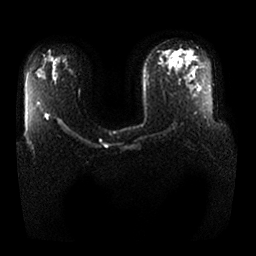
Breast MRI, one axial slice; position 12 of 25 along the scan axis; diffusion-weighted series; image 2 of 4 stored at this slice position (different b-values; order by instance number); 1.5 T; 4 mm slice thickness; 256 × 256 image matrix, field of view 380 × 380 mm. Female patient.
Annotated regions visible in this slice (expert manual segmentation):
- tumour on diffusion-weighted imaging: box from (x=46, y=114) to (x=49, y=118) px